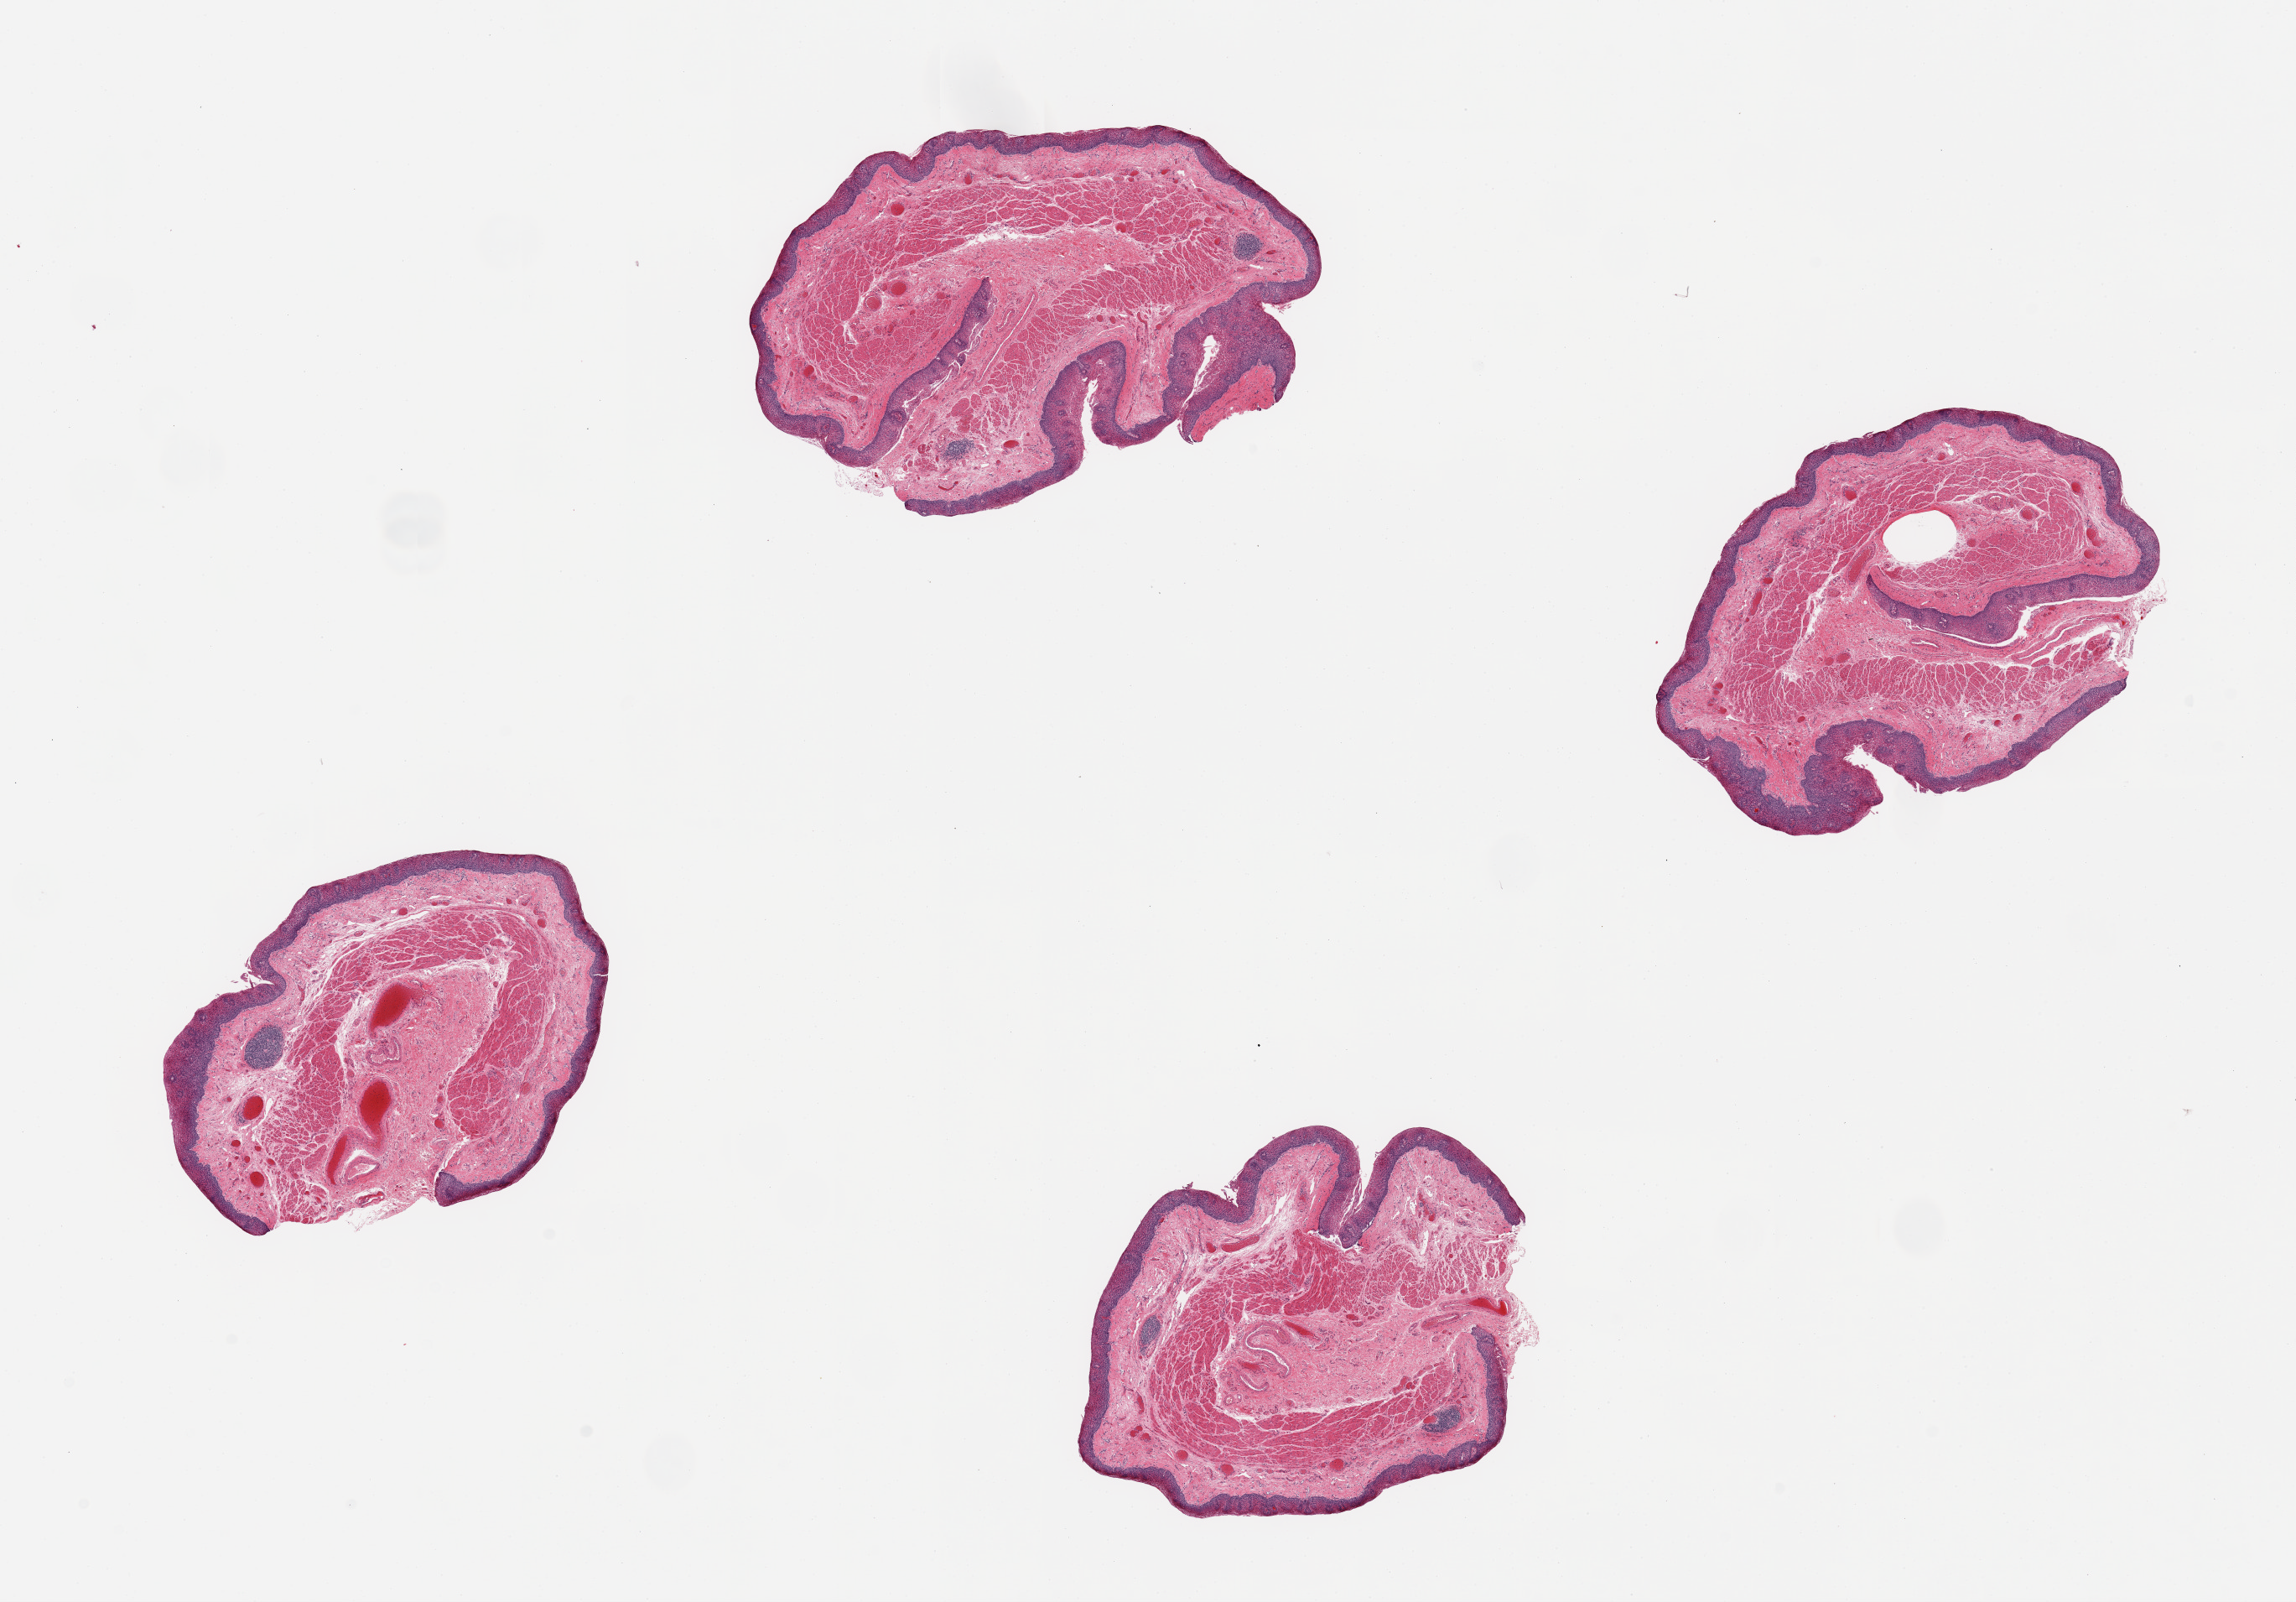
Digitized H&E-stained section — whole scanned area (about 21.7 x 15.1 mm, slide scanned at 20x) shown as a low-resolution overview. PAXgene-fixed, paraffin-embedded tissue. Sampled site (target tissue): esophageal mucous membrane. Tissue donor sample.
• pathologist's review note for this sample: 4 pieces